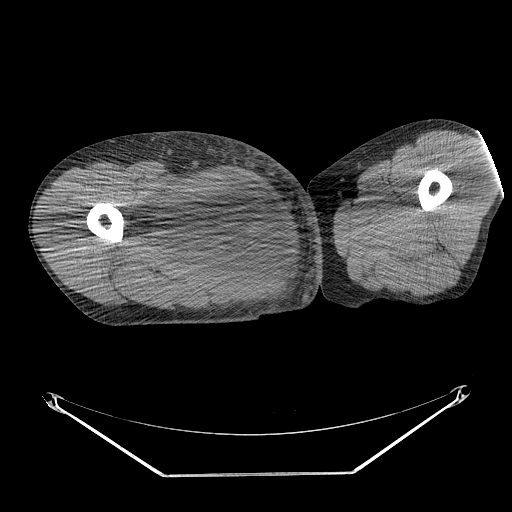
CT of an extremity soft-tissue mass (from a PET/CT study), one axial slice; slice 250 of 311 in the series (ordered by position); reconstruction kernel STANDARD; soft-tissue window (W 400 / L 40 HU); 512 × 512 image matrix, field of view 500 × 500 mm. Male patient. Case-level facts recorded for this patient, not image findings: histological type: undifferentiated - pleiomorphic; grade: high; site of the primary tumour: right thigh.
Structures marked on this image (expert contour drawn on MRI and transferred to this co-registered scan by the dataset authors):
- gross tumour volume including surrounding oedema: bounding box (x1, y1, x2, y2) in pixels: (135, 174, 254, 266)
- gross tumour volume (mass): (155, 174, 254, 266)